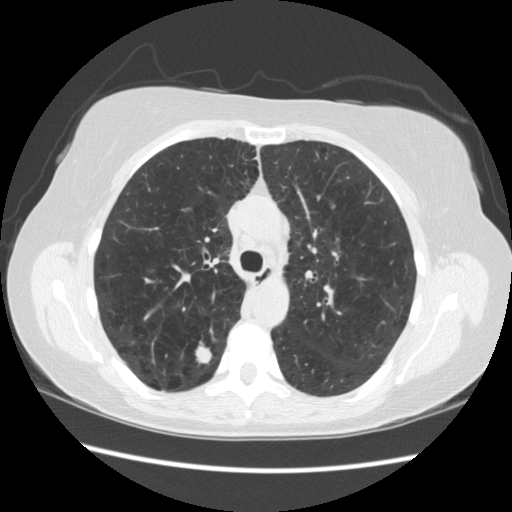
Low-dose screening chest CT, one axial slice. Position 160 of 235 along the scan axis. 120 kVp. Lung window (W 1500 / L -600 HU). 2.5 mm slice thickness. 512 × 512 image matrix.
Outlined on this slice (expert manual segmentation):
- lesion 1 (tumor, upper lobe of right lung): bounding box [x1, y1, x2, y2] px = [195, 338, 212, 362]